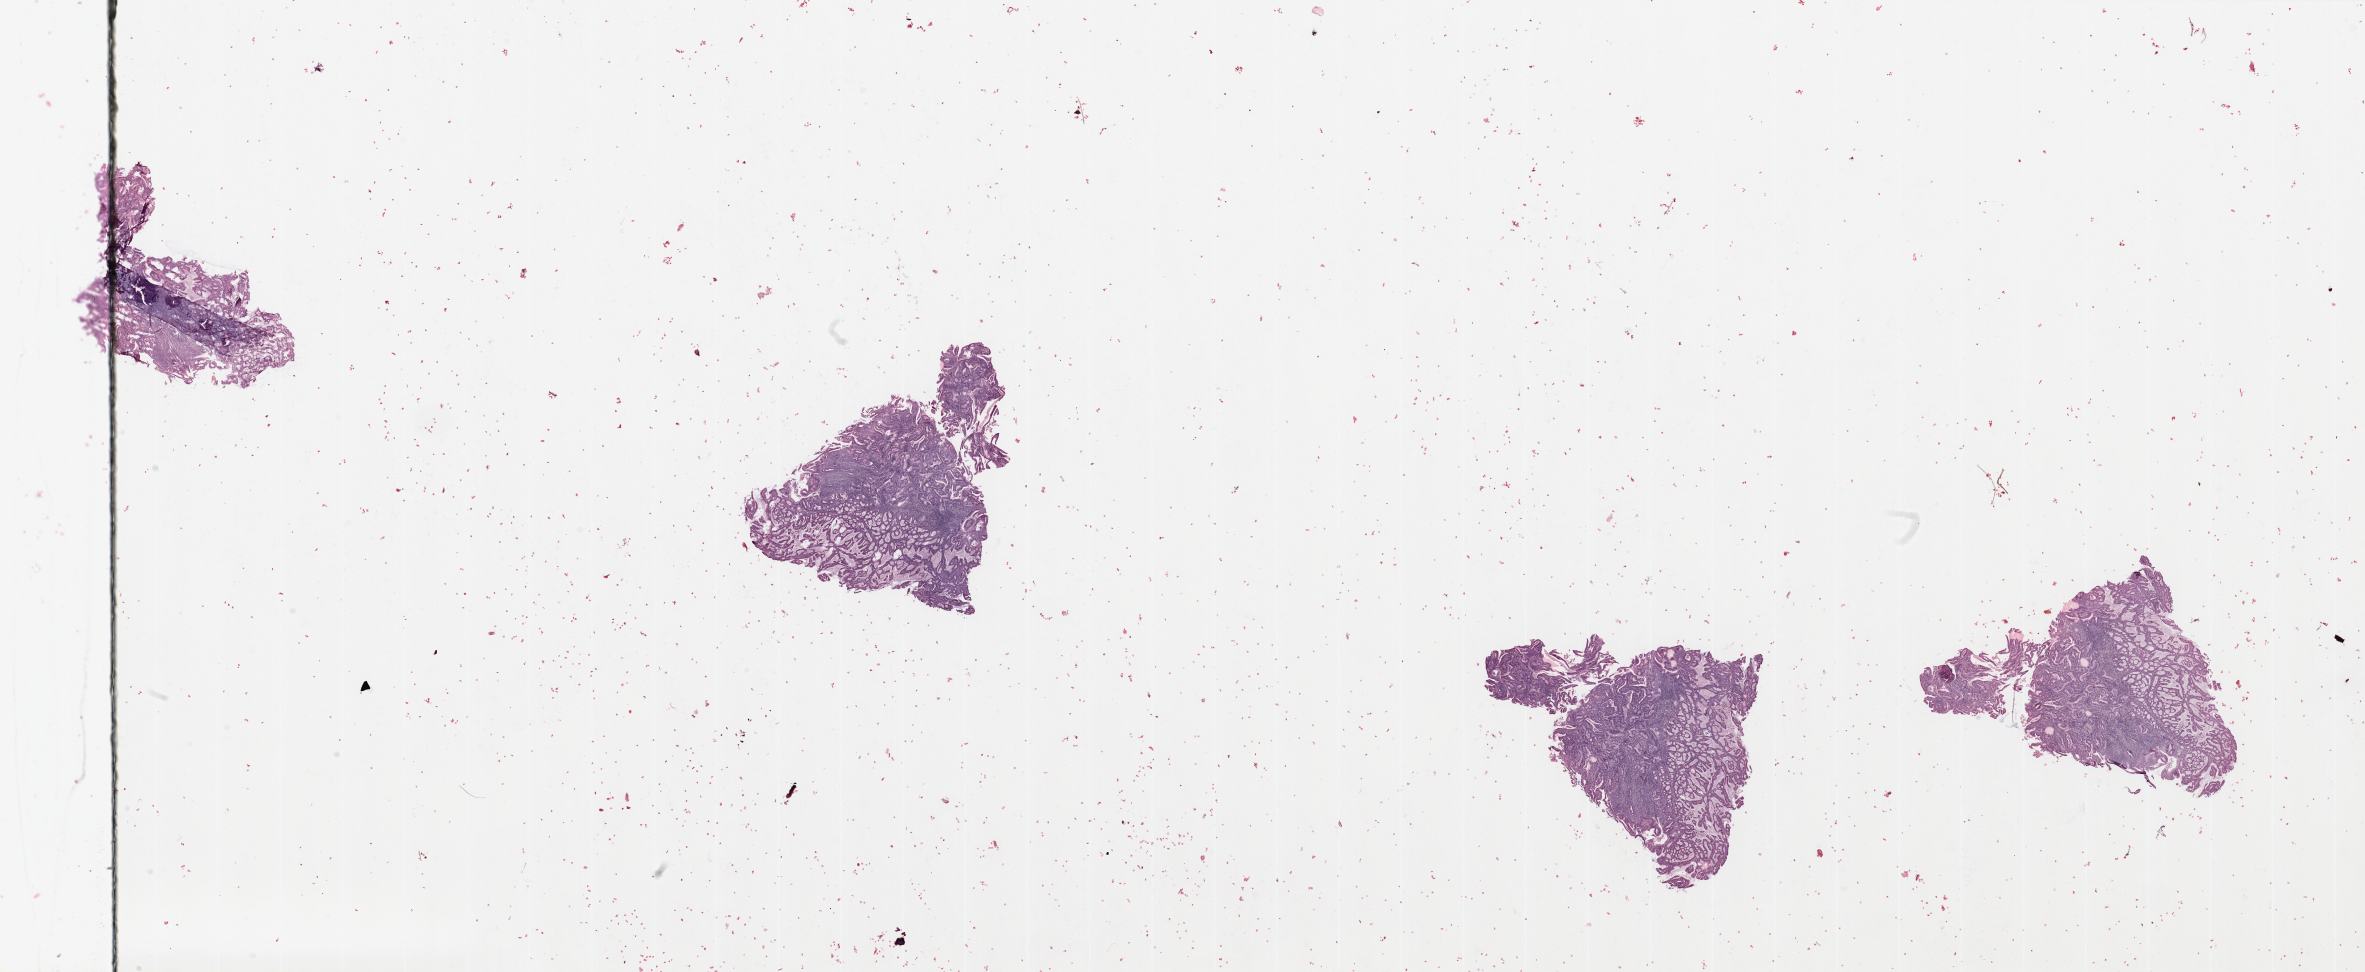
Whole-slide histology image, H&E-stained, a low-resolution overview of the entire scanned area, about 37.4 x 15.4 mm (slide scanned at 20x). Uterus, tumour tissue. 60-year-old female patient.
Diagnosis: Endometrioid adenocarcinoma, NOS.